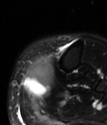
MRI of an extremity soft-tissue mass, one axial slice. Position 21 of 78 along the scan axis. T2-weighted fat-saturated. MR volume resampled by the dataset authors to the PET/CT grid (not the native acquisition matrix). 3.27 mm slice thickness. 107 × 125 image matrix. Female patient. Case-level facts recorded for this patient, not image findings: histological type: extraskeletal high grade osteogenic sarcoma; grade: high; site of the primary tumour: left calf.
Structures marked on this image (expert contour drawn on MRI and transferred to this co-registered scan by the dataset authors):
- gross tumour volume (mass): bounding box (x1, y1, x2, y2) in pixels: (25, 59, 54, 98)